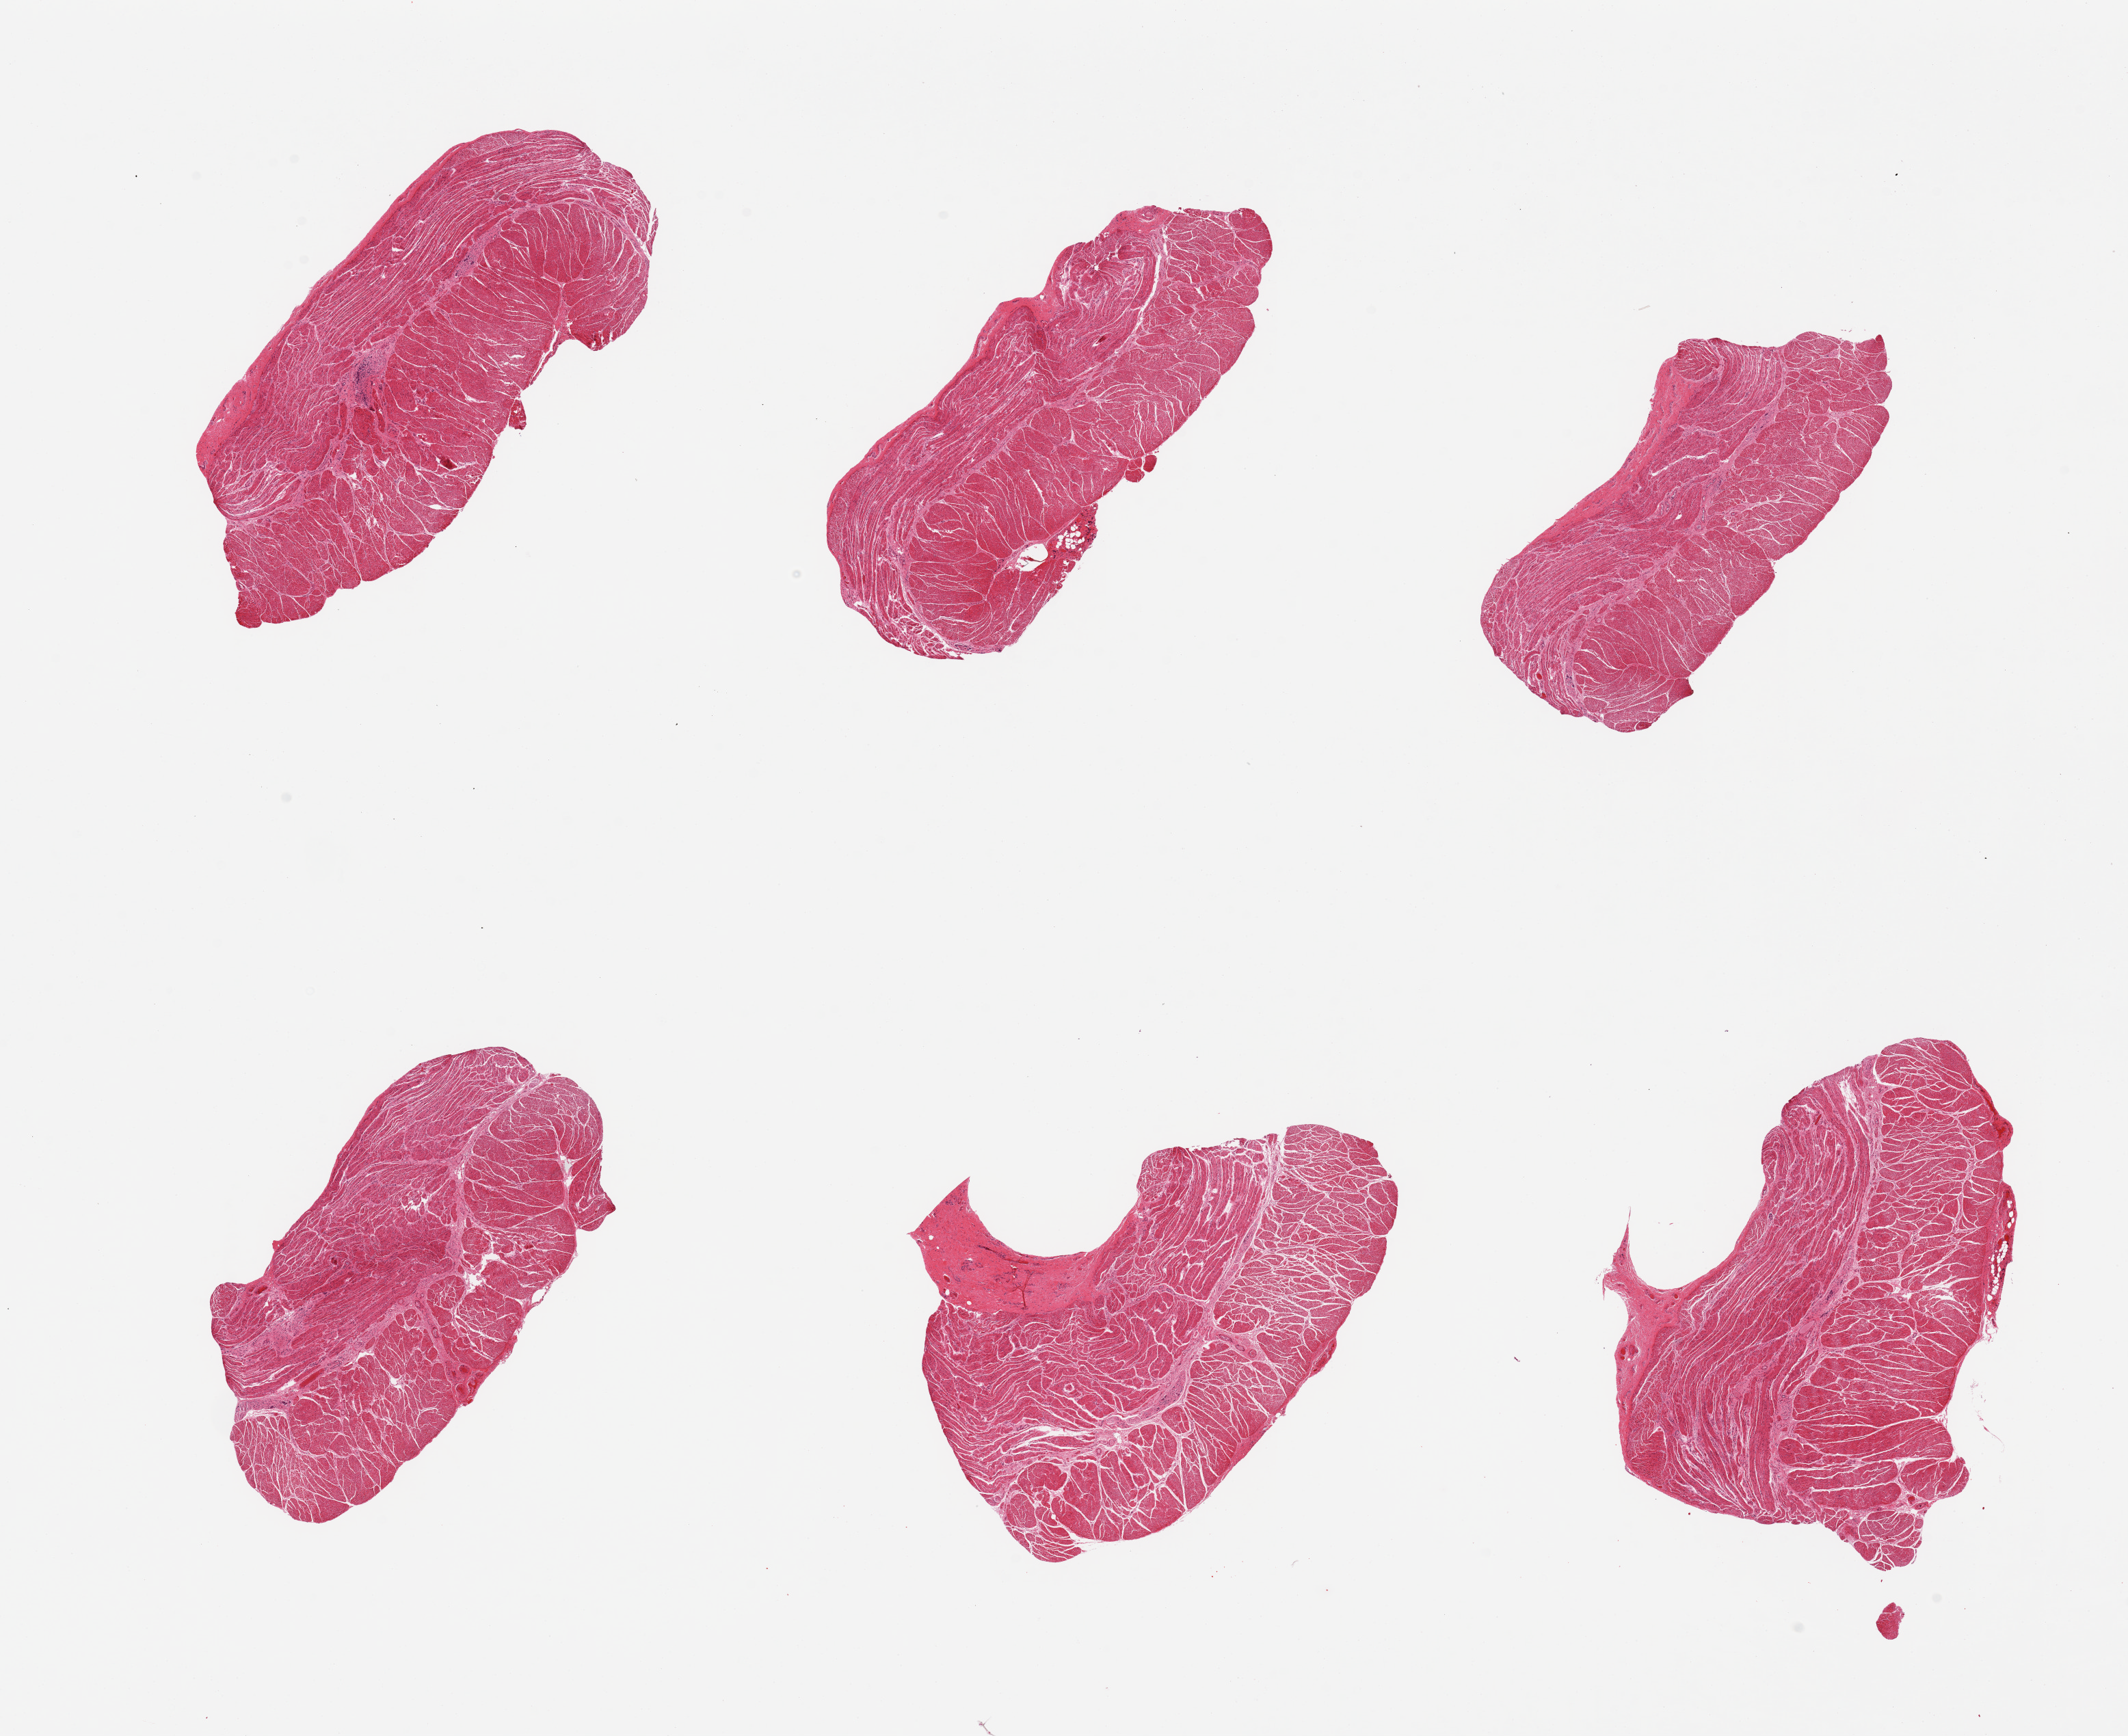
Whole-slide image, haematoxylin and eosin stain, brightfield — shown as a low-resolution overview of the whole scanned area (about 24.6 x 20.1 mm, from a 20x scan). PAXgene-fixed, paraffin-embedded tissue. Target tissue: esophageal muscle. Tissue donor sample. Donor: male.
* reviewer comment on this tissue sample: 6 pieces. Well dissected